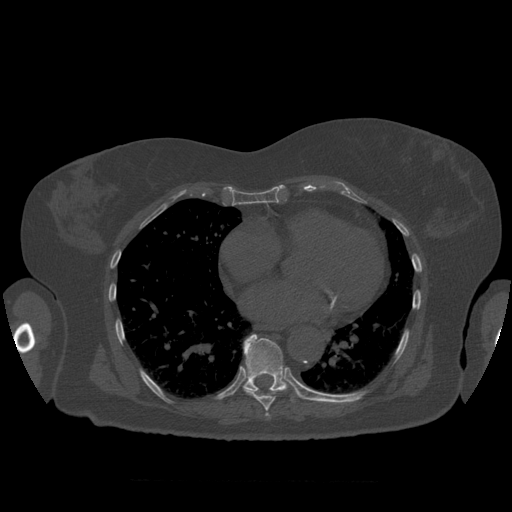
CT including the spine, one axial slice; position 369 of 399 along the scan axis; reconstruction kernel STANDARD; 120 kVp; bone window (W 1800 / L 400 HU); 1.25 mm slice thickness; 512 × 512 image matrix, field of view 404 × 404 mm. Patient age 81 years. From the clinical record (not read from this slice): primary cancer: renal.
Annotated regions visible in this slice (semi-automatically segmented with operator editing):
- T7 vertebra: bounding box (x1, y1, x2, y2) in pixels: (265, 413, 270, 417)
- T8 vertebra: (244, 389, 278, 411)
- T9 vertebra: (244, 334, 302, 402)